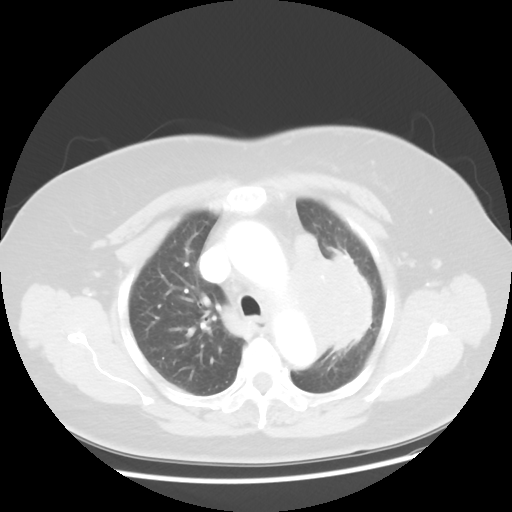
Chest CT, one axial slice; 120 kVp; lung window (W 1500 / L -600 HU); 5 mm slice thickness; 512 × 512 image matrix, field of view 374 × 374 mm. Patient: female, 58 years. Case-level facts recorded for this patient, not image findings: clinical TNM (as recorded): T4 N3 M0; histopathological grade: G3.
Outlined on this slice (bounding box drawn by a radiologist):
- lung tumour (recorded histology: small cell carcinoma): bounding box [x1, y1, x2, y2] px = [284, 227, 380, 373]